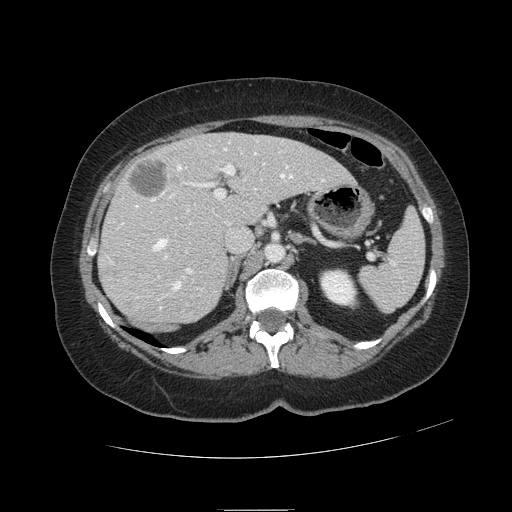
Contrast-enhanced abdominal CT, one axial slice; position 66 of 121 along the scan axis; 120 kVp; intravenous contrast given; soft-tissue window (W 400 / L 40 HU); 512 × 512 image matrix, field of view 400 × 400 mm. Female patient, age 52 years. From the clinical record (not read from this slice): diagnosis: colorectal cancer liver metastases, imaged before liver resection; multiple liver metastases: yes; largest metastasis: 6.3 cm; chemotherapy before resection: yes.
Structures marked on this image (manually delineated by an expert):
- hepatic veins: bounding box [x1, y1, x2, y2] px = [136, 142, 325, 310]
- liver: [100, 134, 352, 324]
- planned liver remnant (the part of the liver to remain after resection): [167, 134, 353, 224]
- portal vein (with intrahepatic branches): [122, 151, 281, 278]
- liver metastasis: [129, 160, 167, 196]